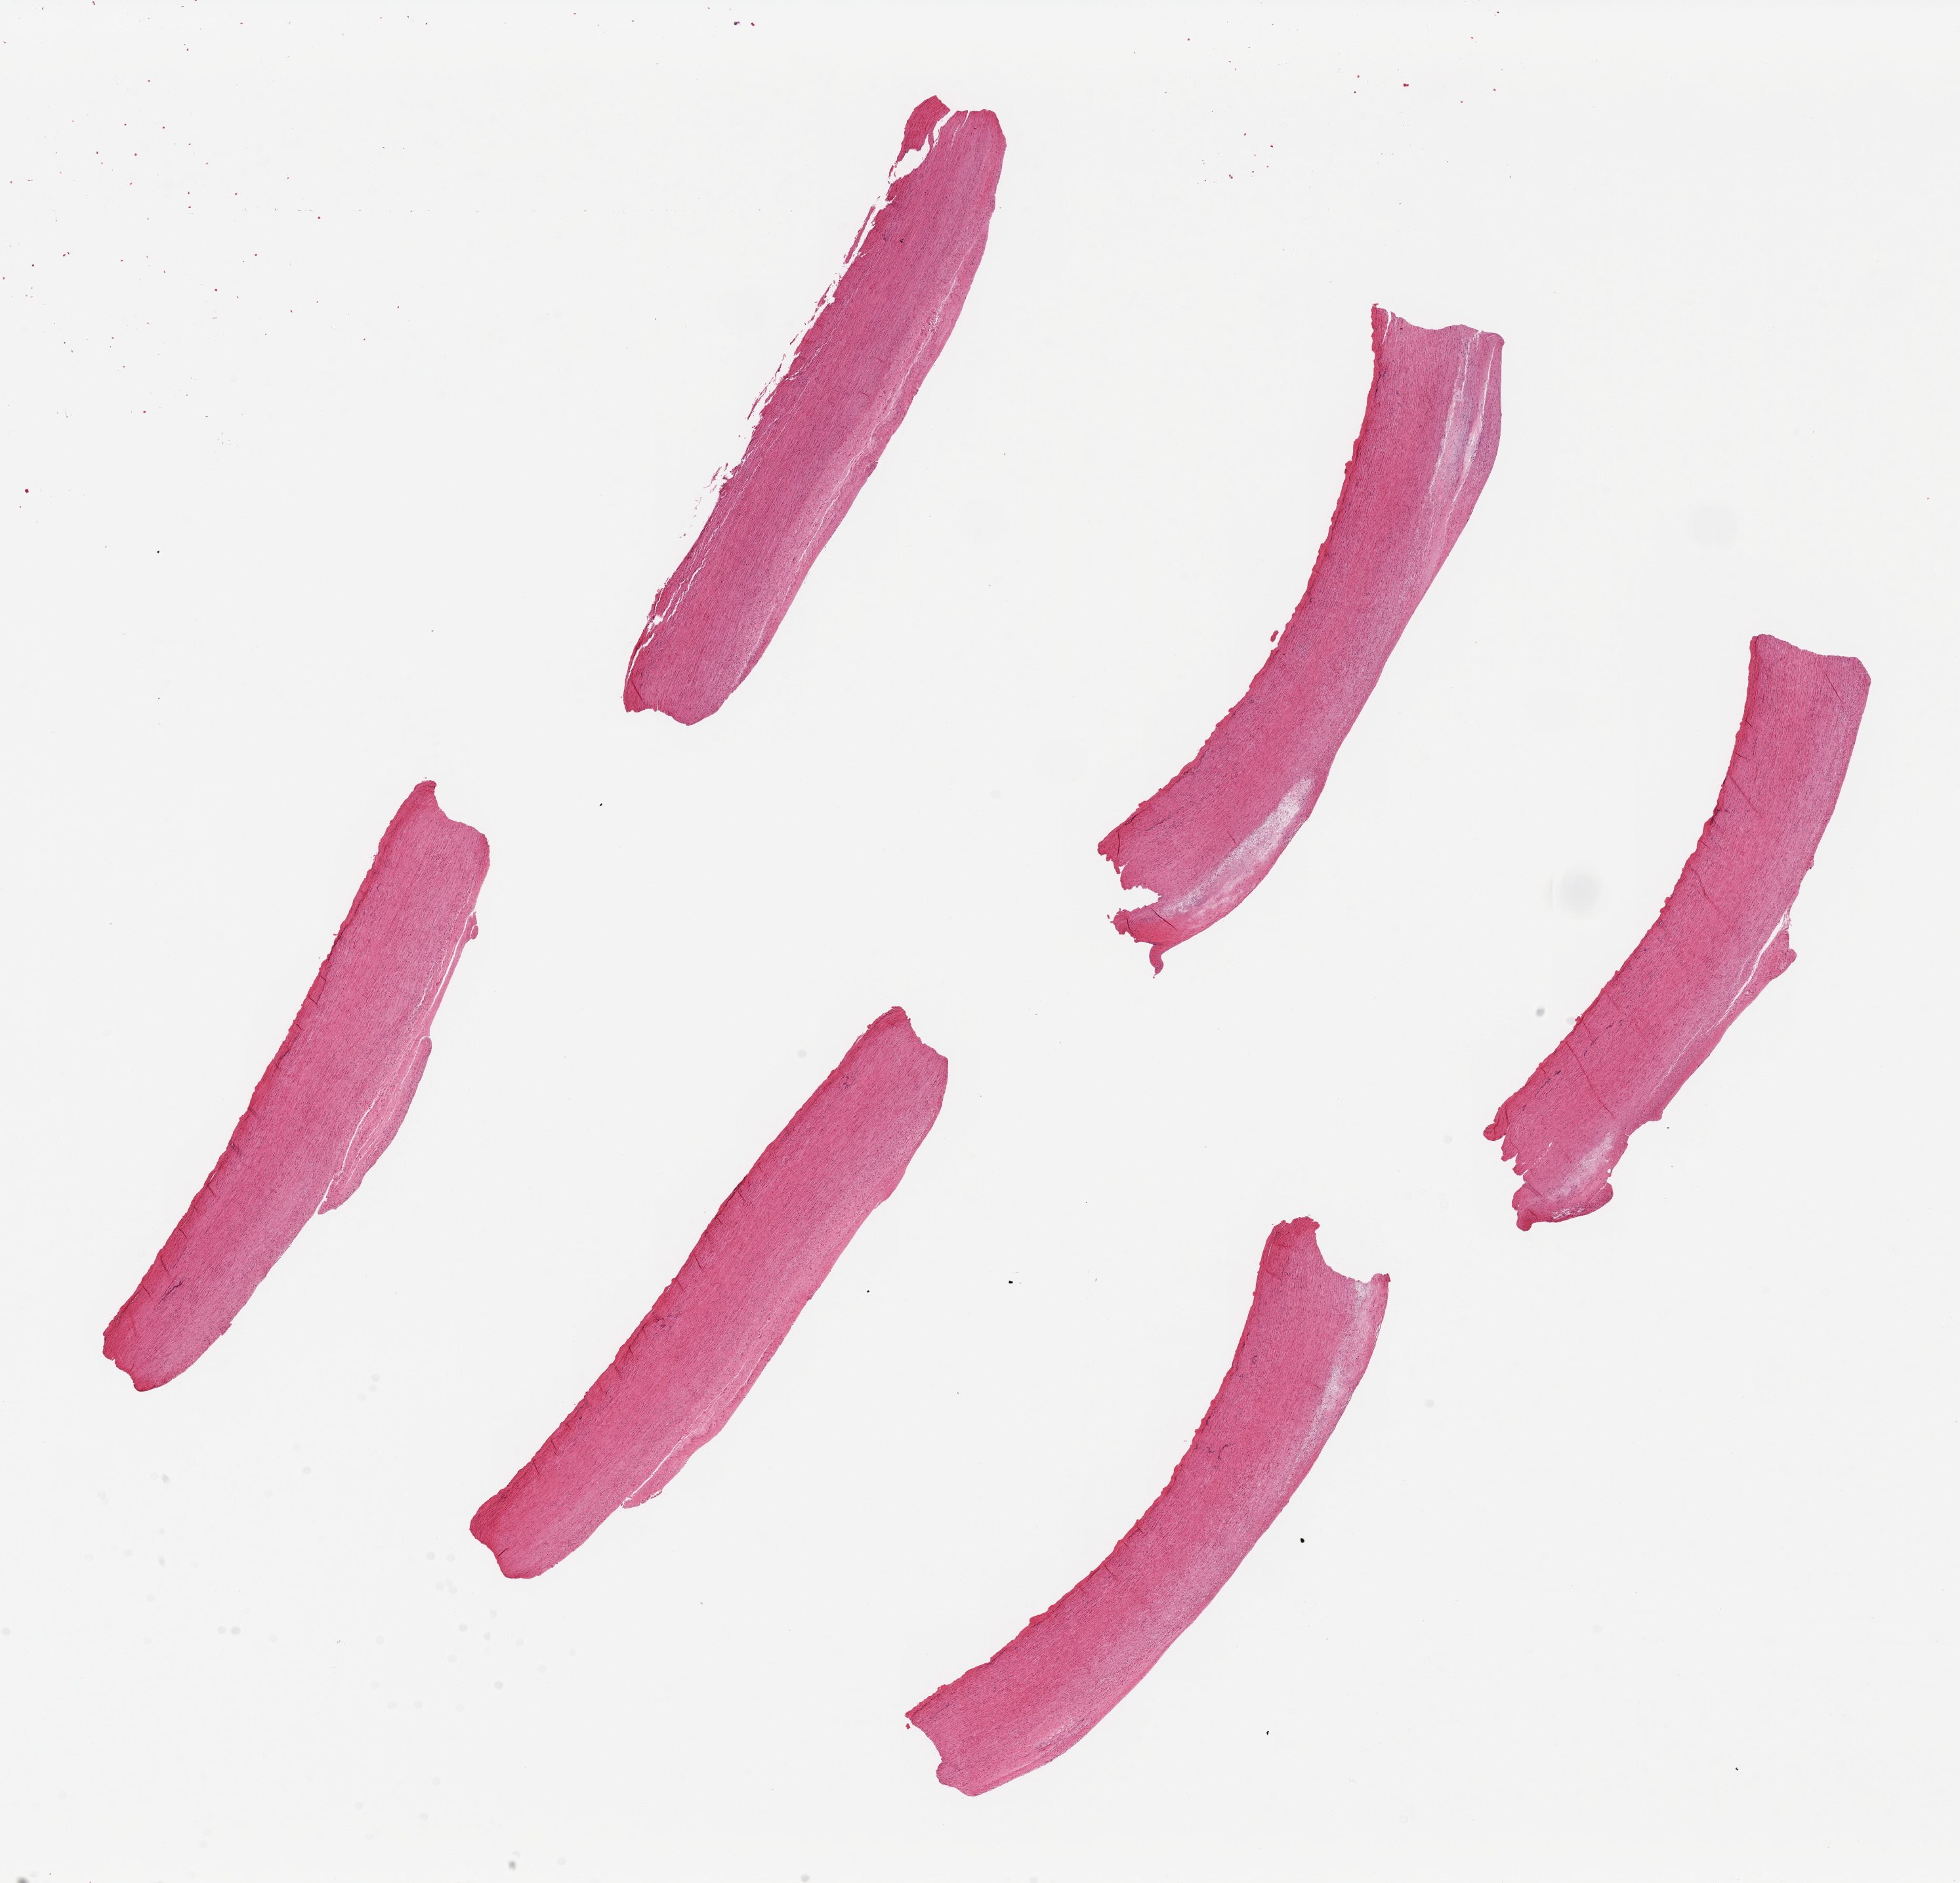
Hematoxylin and eosin (H&E) whole-slide image, low-resolution overview of the scanned area, about 23.6 x 22.7 mm (acquisition: 20x scan). PAXgene-fixed paraffin-embedded (PFPE) section. Target tissue: aorta. Tissue donor sample. Male donor.
* reviewer comment on this tissue sample: 6 pieces ~8x1.5mm. Mild patchy atherosis